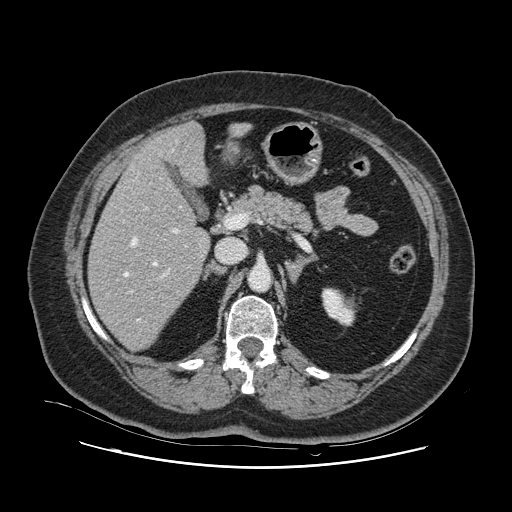
Contrast-enhanced abdominal CT, one axial slice; slice 57 of 132 in the series (ordered by position); intravenous contrast given; soft-tissue window (W 400 / L 40 HU); 2.5 mm slice thickness; 512 × 512 image matrix, field of view 391 × 391 mm. Female patient, age 73 years. From the clinical record (not read from this slice): diagnosis: colorectal cancer liver metastases, imaged before liver resection; multiple liver metastases: no; largest metastasis: 7 cm; disease in both lobes: no.
Structures marked on this image (outlined manually by an expert reader):
- hepatic veins: bounding box (x1, y1, x2, y2) in pixels: (123, 150, 182, 322)
- liver: (90, 124, 210, 350)
- planned liver remnant (the part of the liver to remain after resection): (90, 148, 210, 350)
- portal vein (with intrahepatic branches): (129, 229, 186, 293)